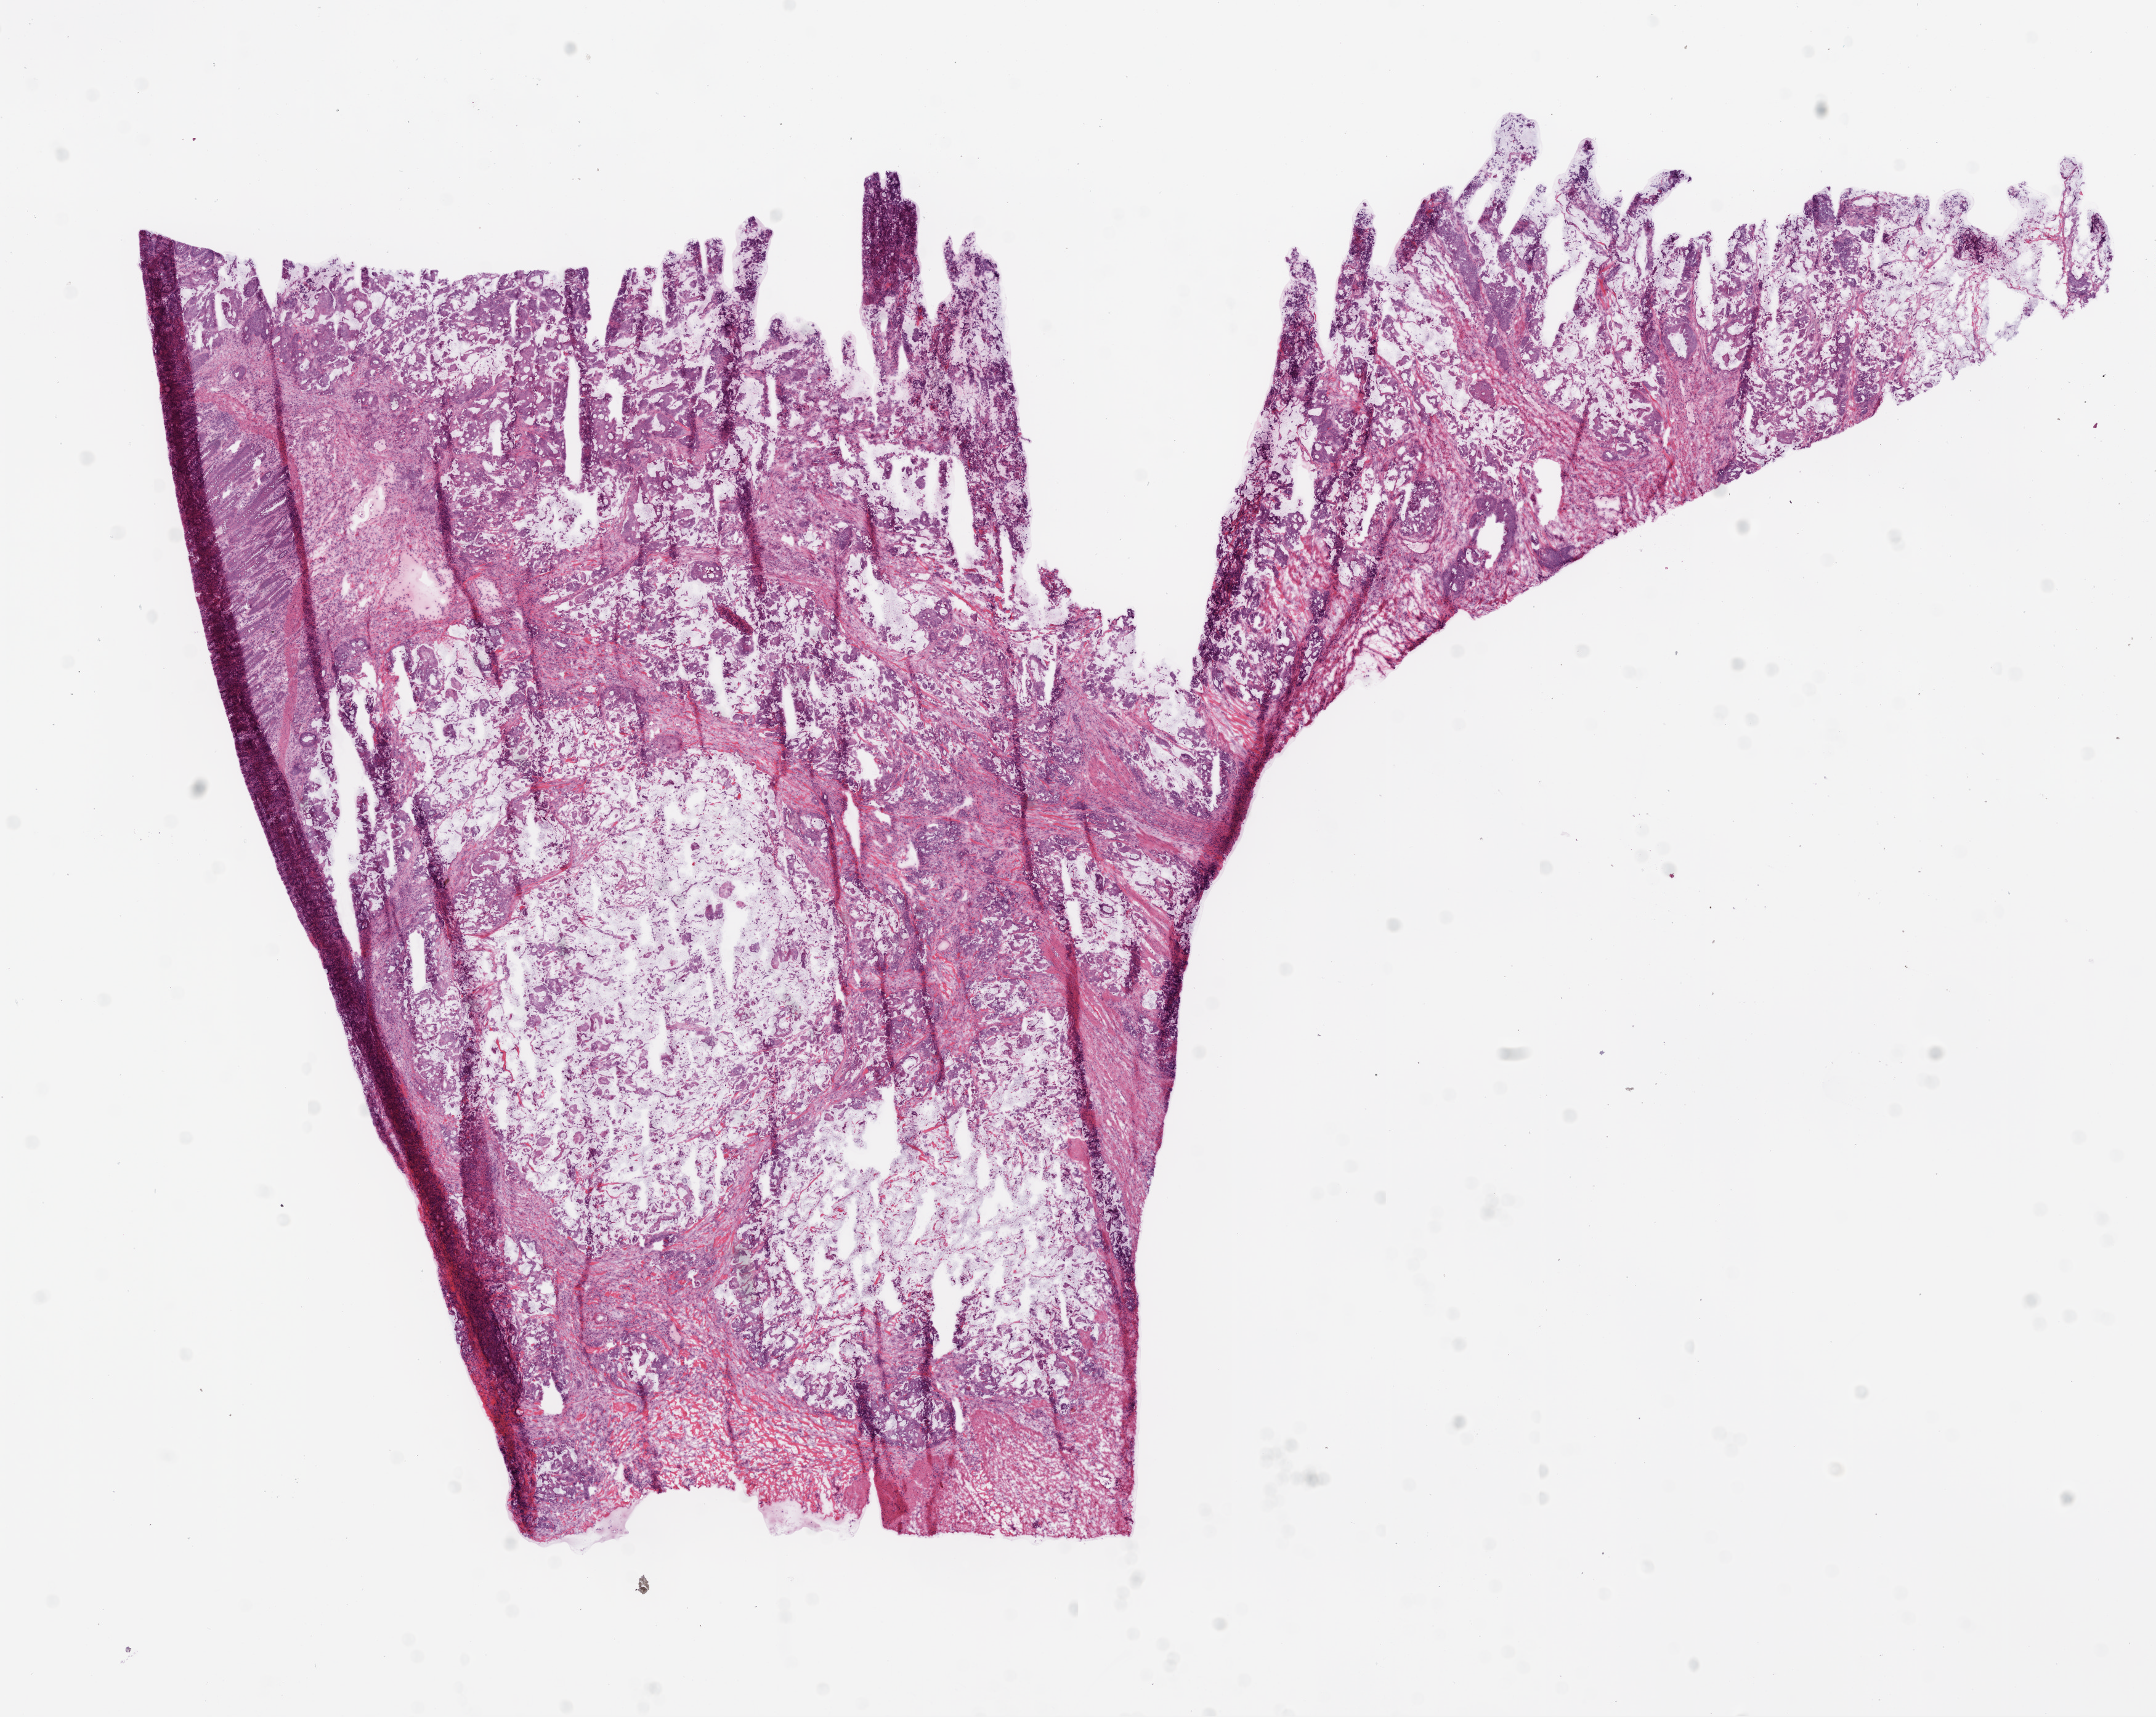
H&E whole-slide image — shown as a low-resolution overview of the whole scanned area (about 14.0 x 11.2 mm); frozen section; sample: primary tumour, colon. Female patient; age at initial diagnosis 64 years. Pathologist review of this section (percent, as recorded): tumour cells 70%, tumour nuclei 70%, normal cells 5%, stromal cells 25%, necrosis 0%.
Lymph nodes positive (case pathology): 9 of 10 examined. TNM: T4 N2 M1. AJCC pathologic stage: IV (5th edition). Pathologic diagnosis: Mucinous adenocarcinoma (cecum).